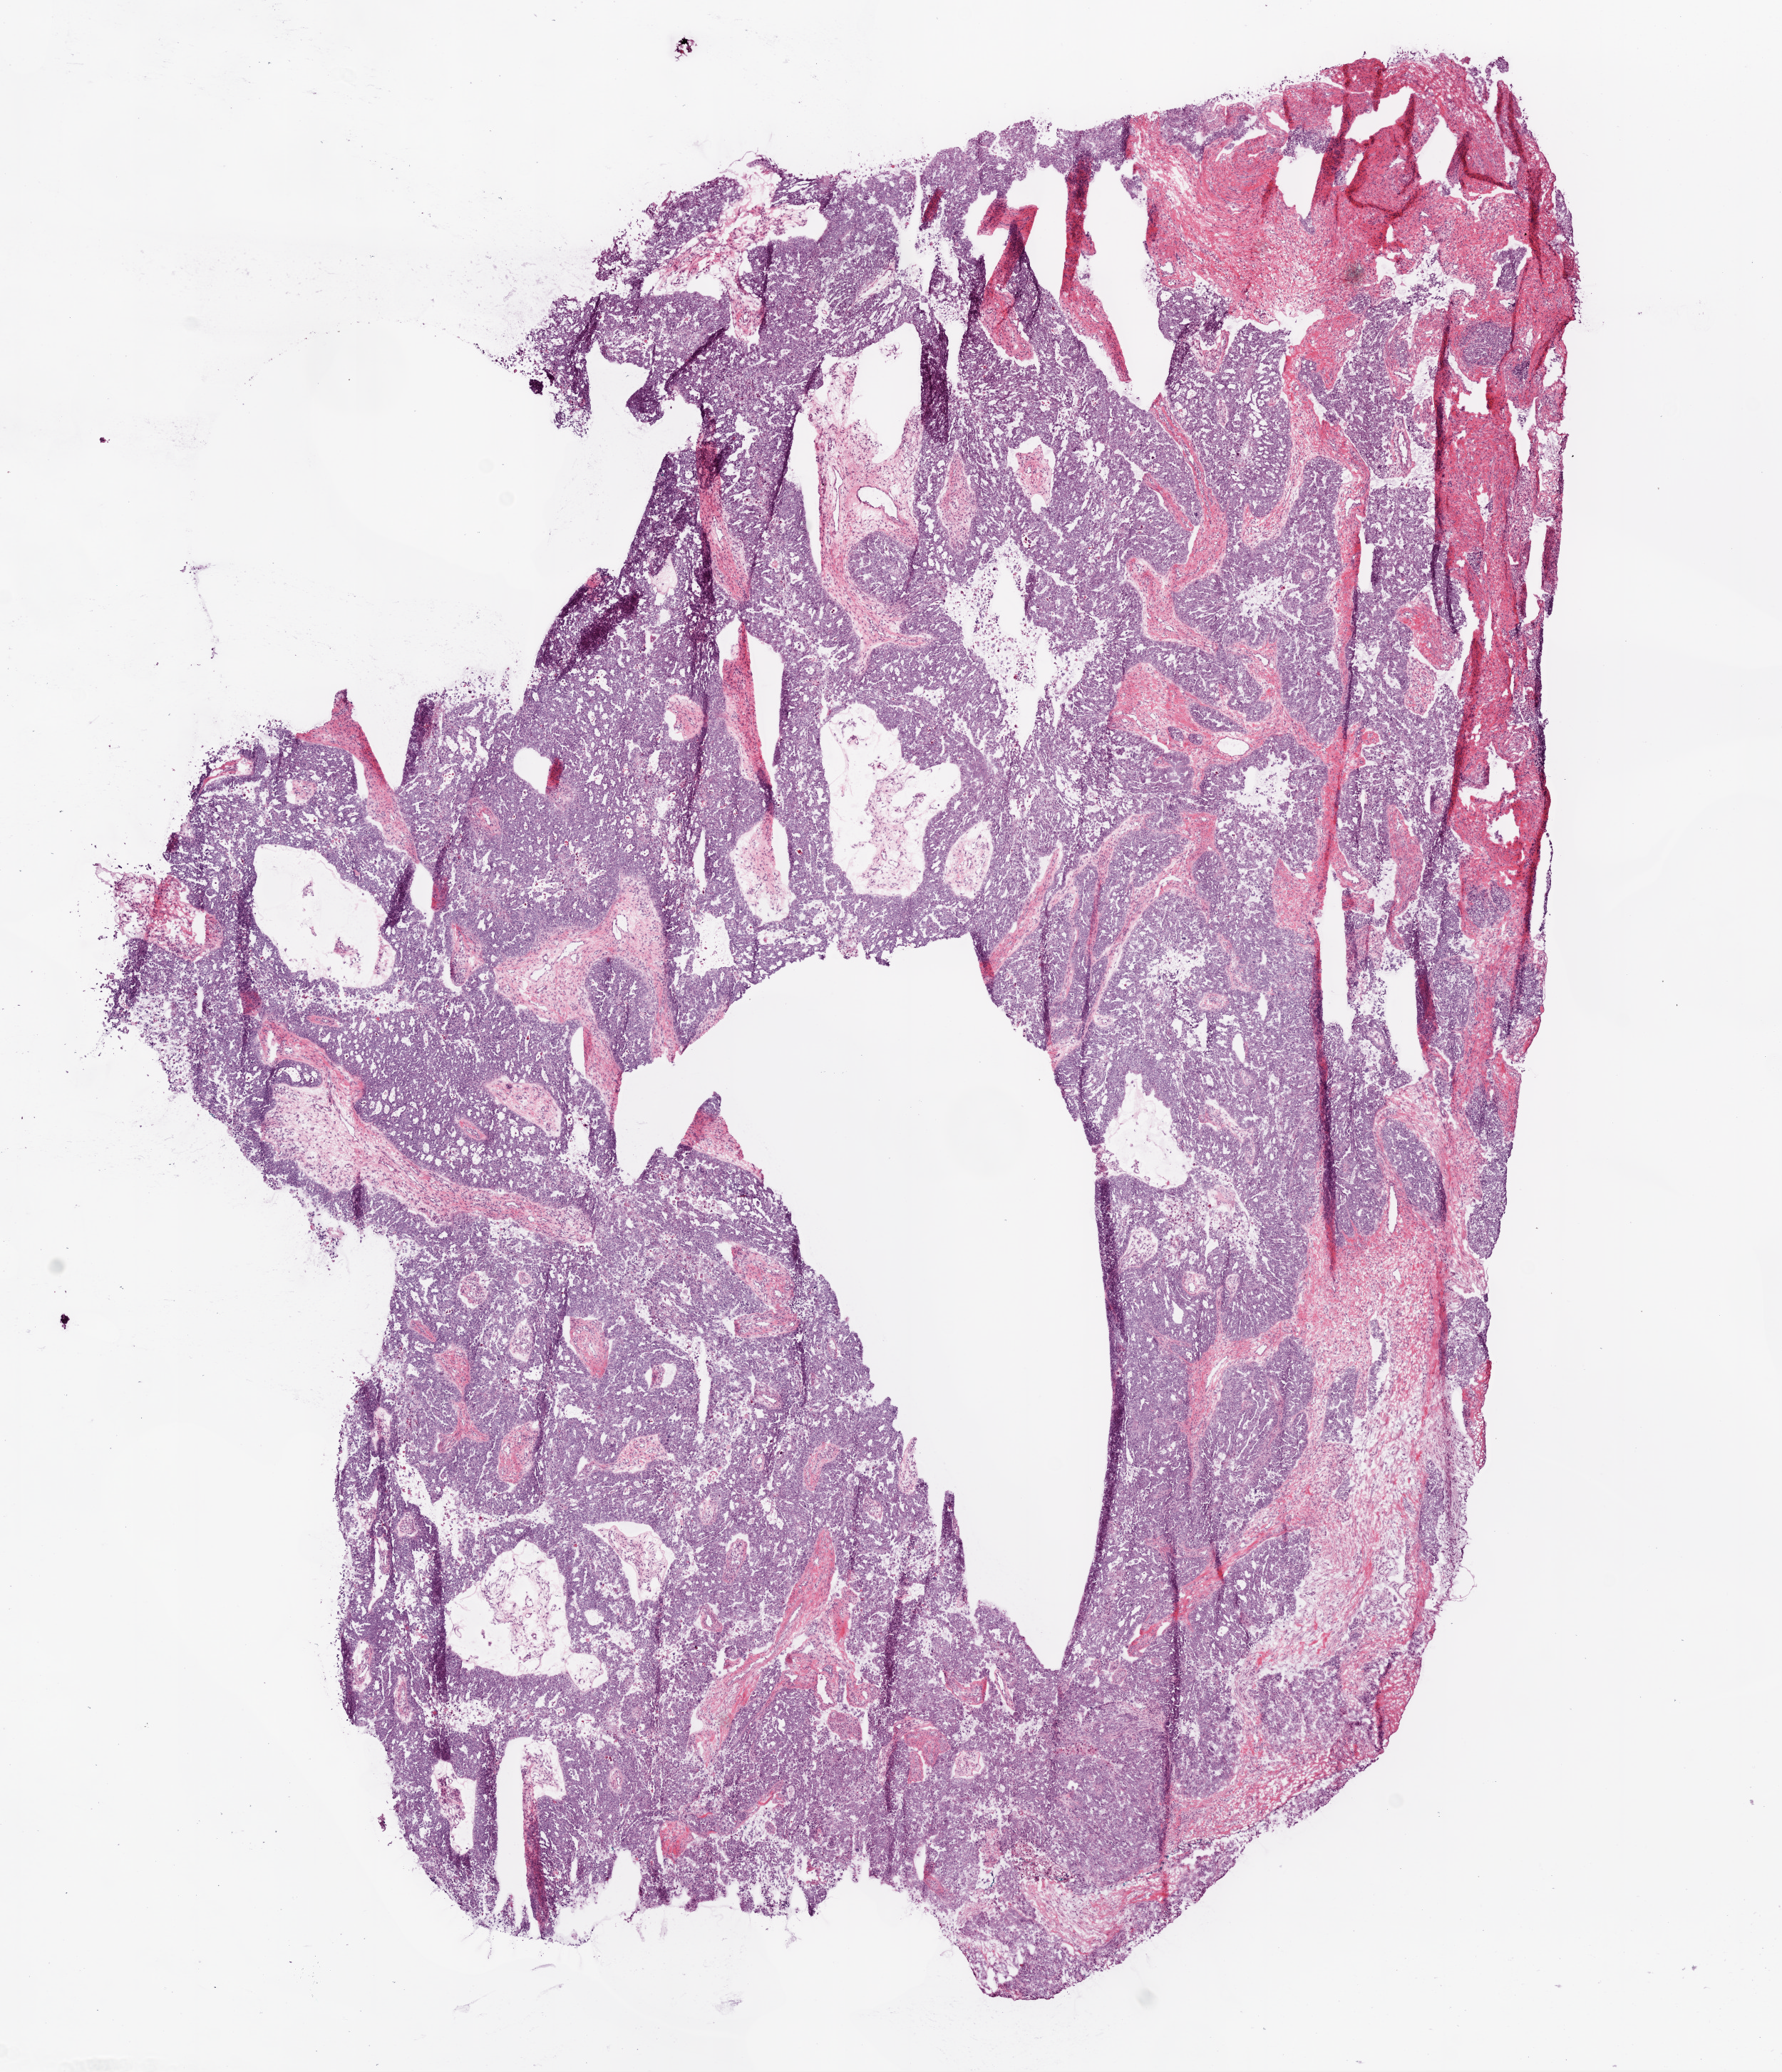
Hematoxylin and eosin (H&E) stained whole-slide image — whole scanned area (about 10.0 x 11.7 mm, slide scanned at 20x) shown as a low-resolution overview; frozen section from the bottom of the tissue portion; sample: primary tumour, ovary. Patient: female, age at initial diagnosis 51 years. Histologic grade: G3 (poorly differentiated). Pathologist review of this section (percent, as recorded): tumour cells 80%, tumour nuclei 95%, normal cells 0%, stromal cells 18%, necrosis 2%.
• laterality: bilateral
• pathologic diagnosis: Serous cystadenocarcinoma, NOS
• FIGO stage: IIIC